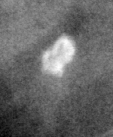
Region of interest cut from a scanned film mammogram (one marked finding); right breast; CC view.
- Marked abnormality: calcifications, morphology lucent center; BI-RADS assessment category 2; benign without callback (not worked up further).